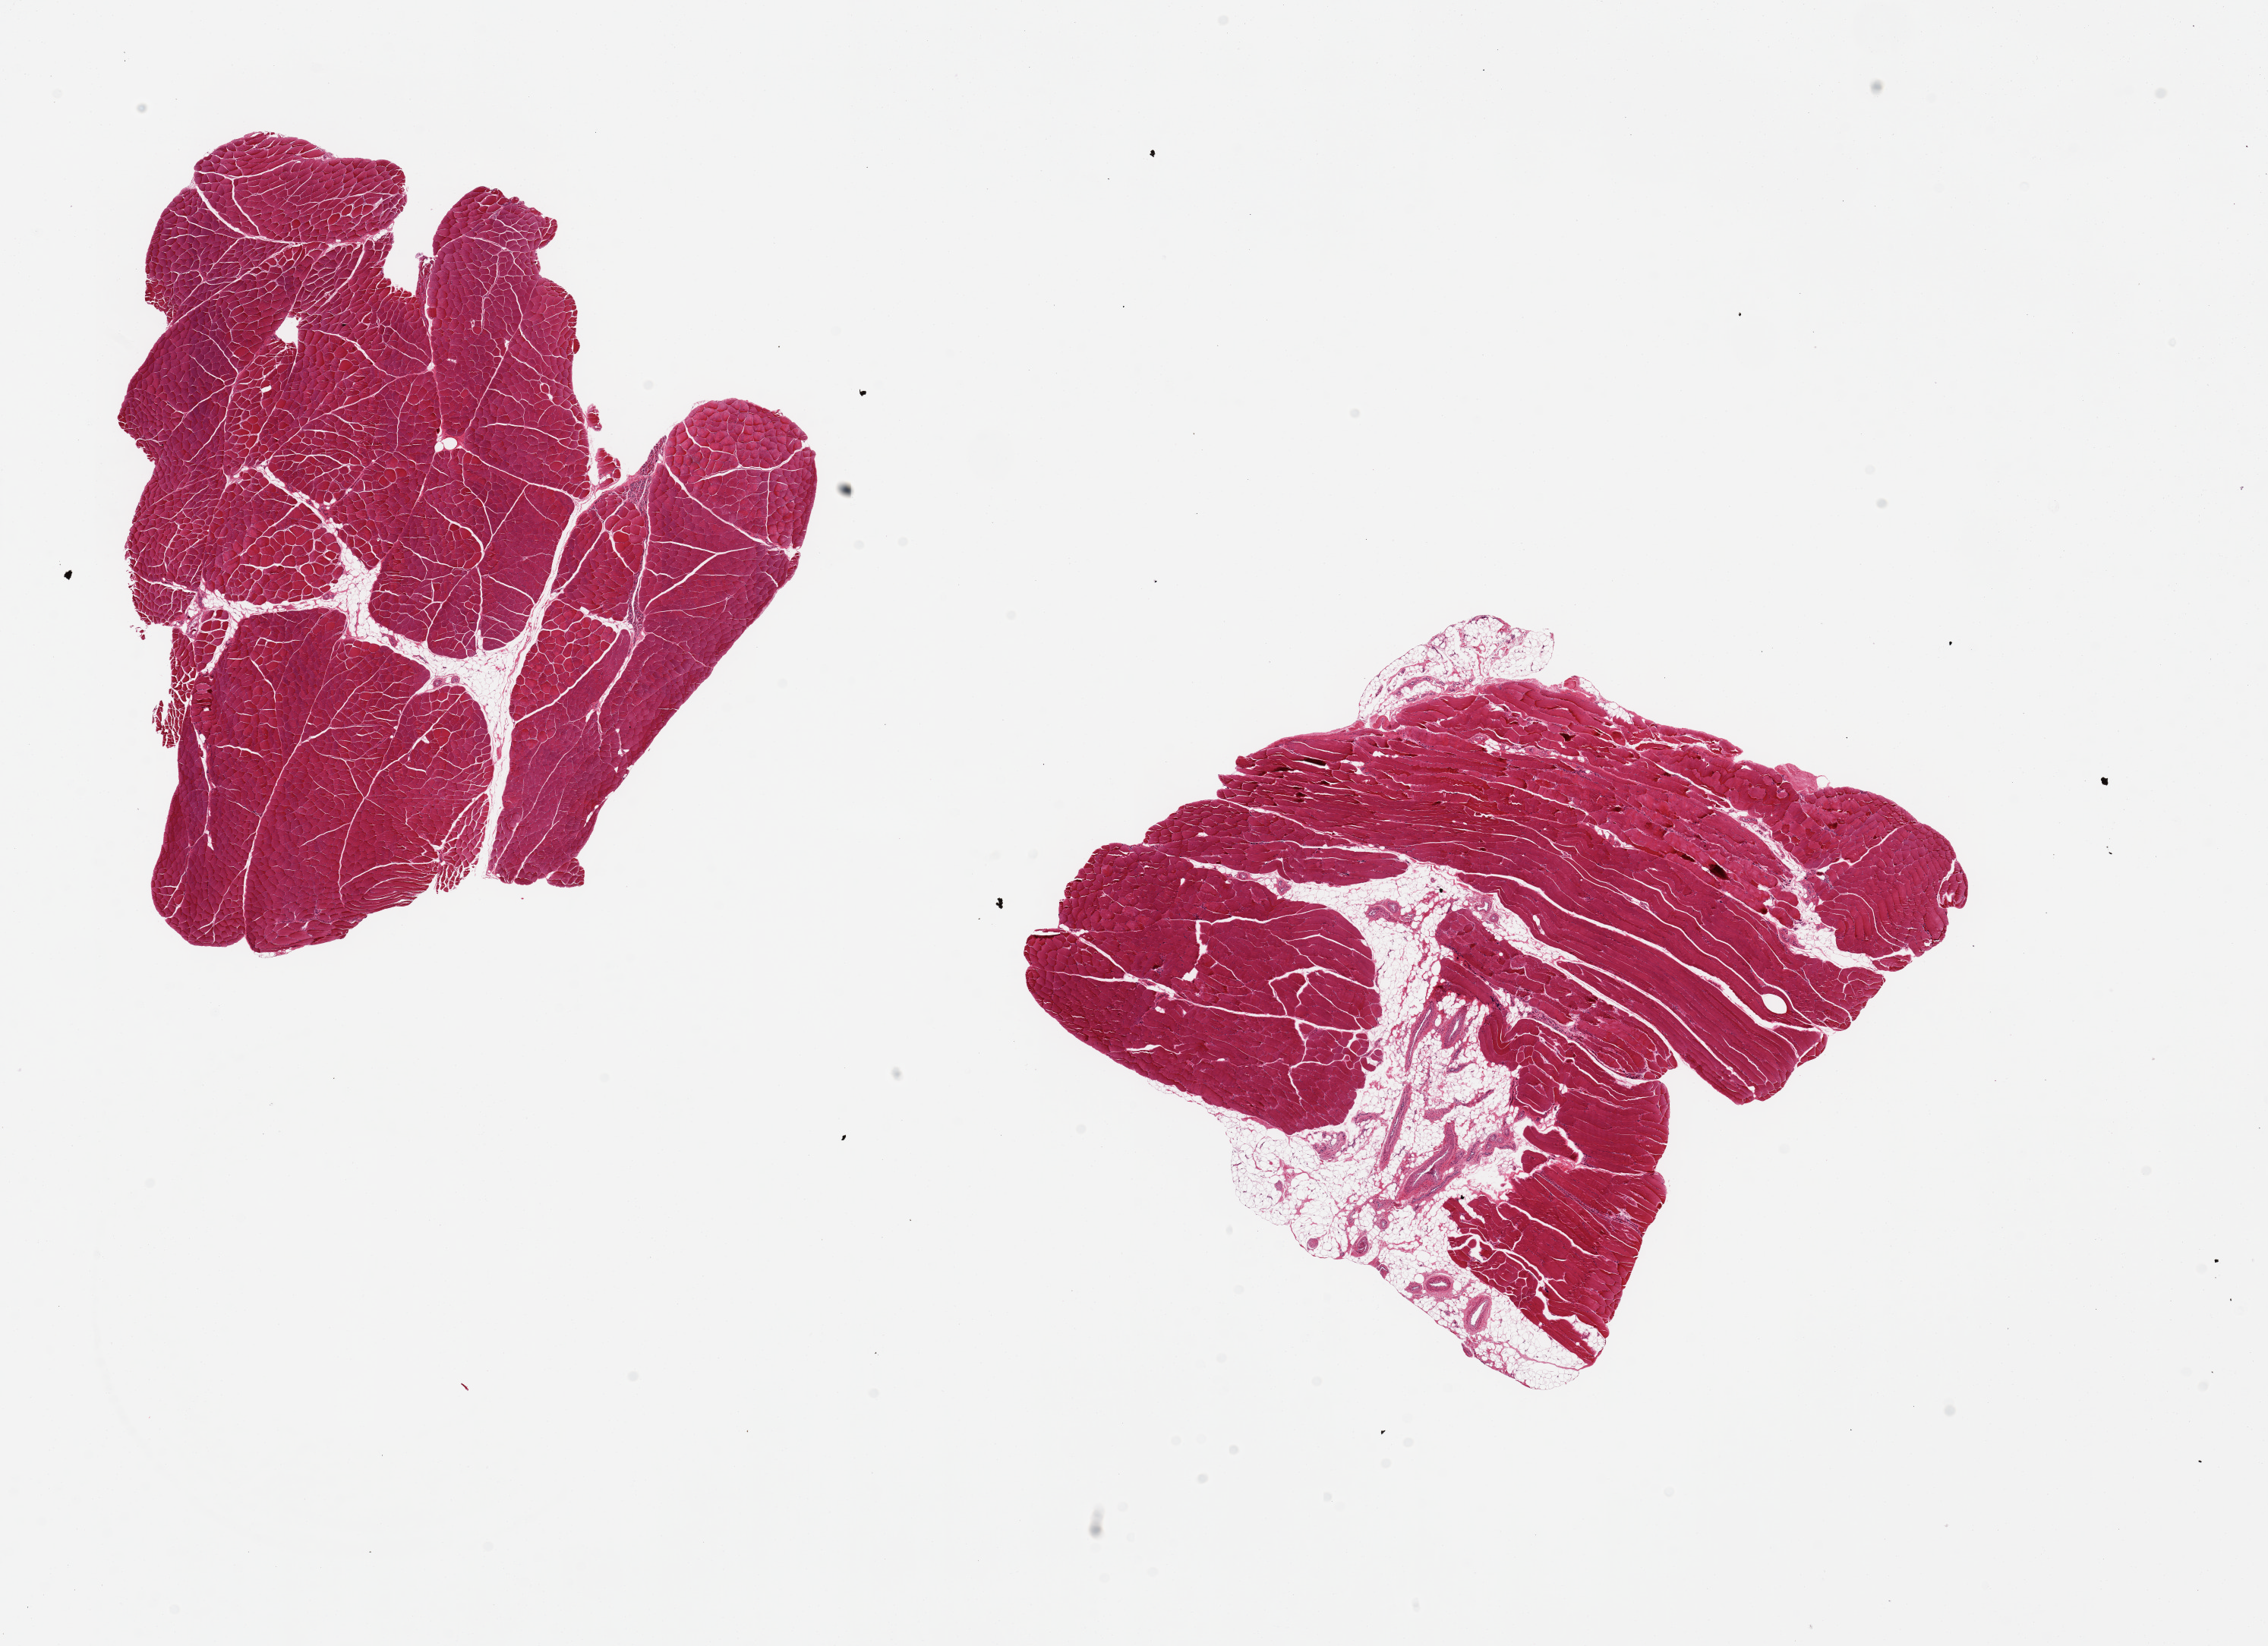
H&E whole-slide image, a low-resolution overview of the entire scanned area, about 23.6 x 17.1 mm (slide scanned at 20x); PAXgene-fixed paraffin-embedded (PFPE) section; section of skeletal muscle (target tissue); tissue donor sample. Female donor.
Review note (as recorded): 2 pieces, 9x7 & 10x8mm; 1 piece has 25% internal adipose.